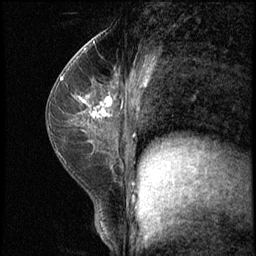
Breast MRI (dynamic contrast-enhanced), one sagittal slice; position 34 of 62 along the scan axis; 3 images stored at this slice position (order not interpretable as contrast timing); 1.5 T; TE 4.2 ms, TR 8.7 ms; 2.5 mm slice thickness; 256 × 256 image matrix. Patient: female, 35 years. From the clinical record (not read from this slice): setting: breast cancer imaged before/during neoadjuvant chemotherapy; receptor status: HER2-positive.
Structures marked on this image (semi-automatic segmentation, software-assisted and operator-edited):
- analysis volume of interest (the breast-tissue region the enhancement analysis was run in; not a lesion): box from (x=71, y=78) to (x=120, y=139) px
- tumour enhancement mask (voxels above the 140 % enhancement threshold inside the analysis volume of interest): (x=75, y=96)–(x=111, y=118)